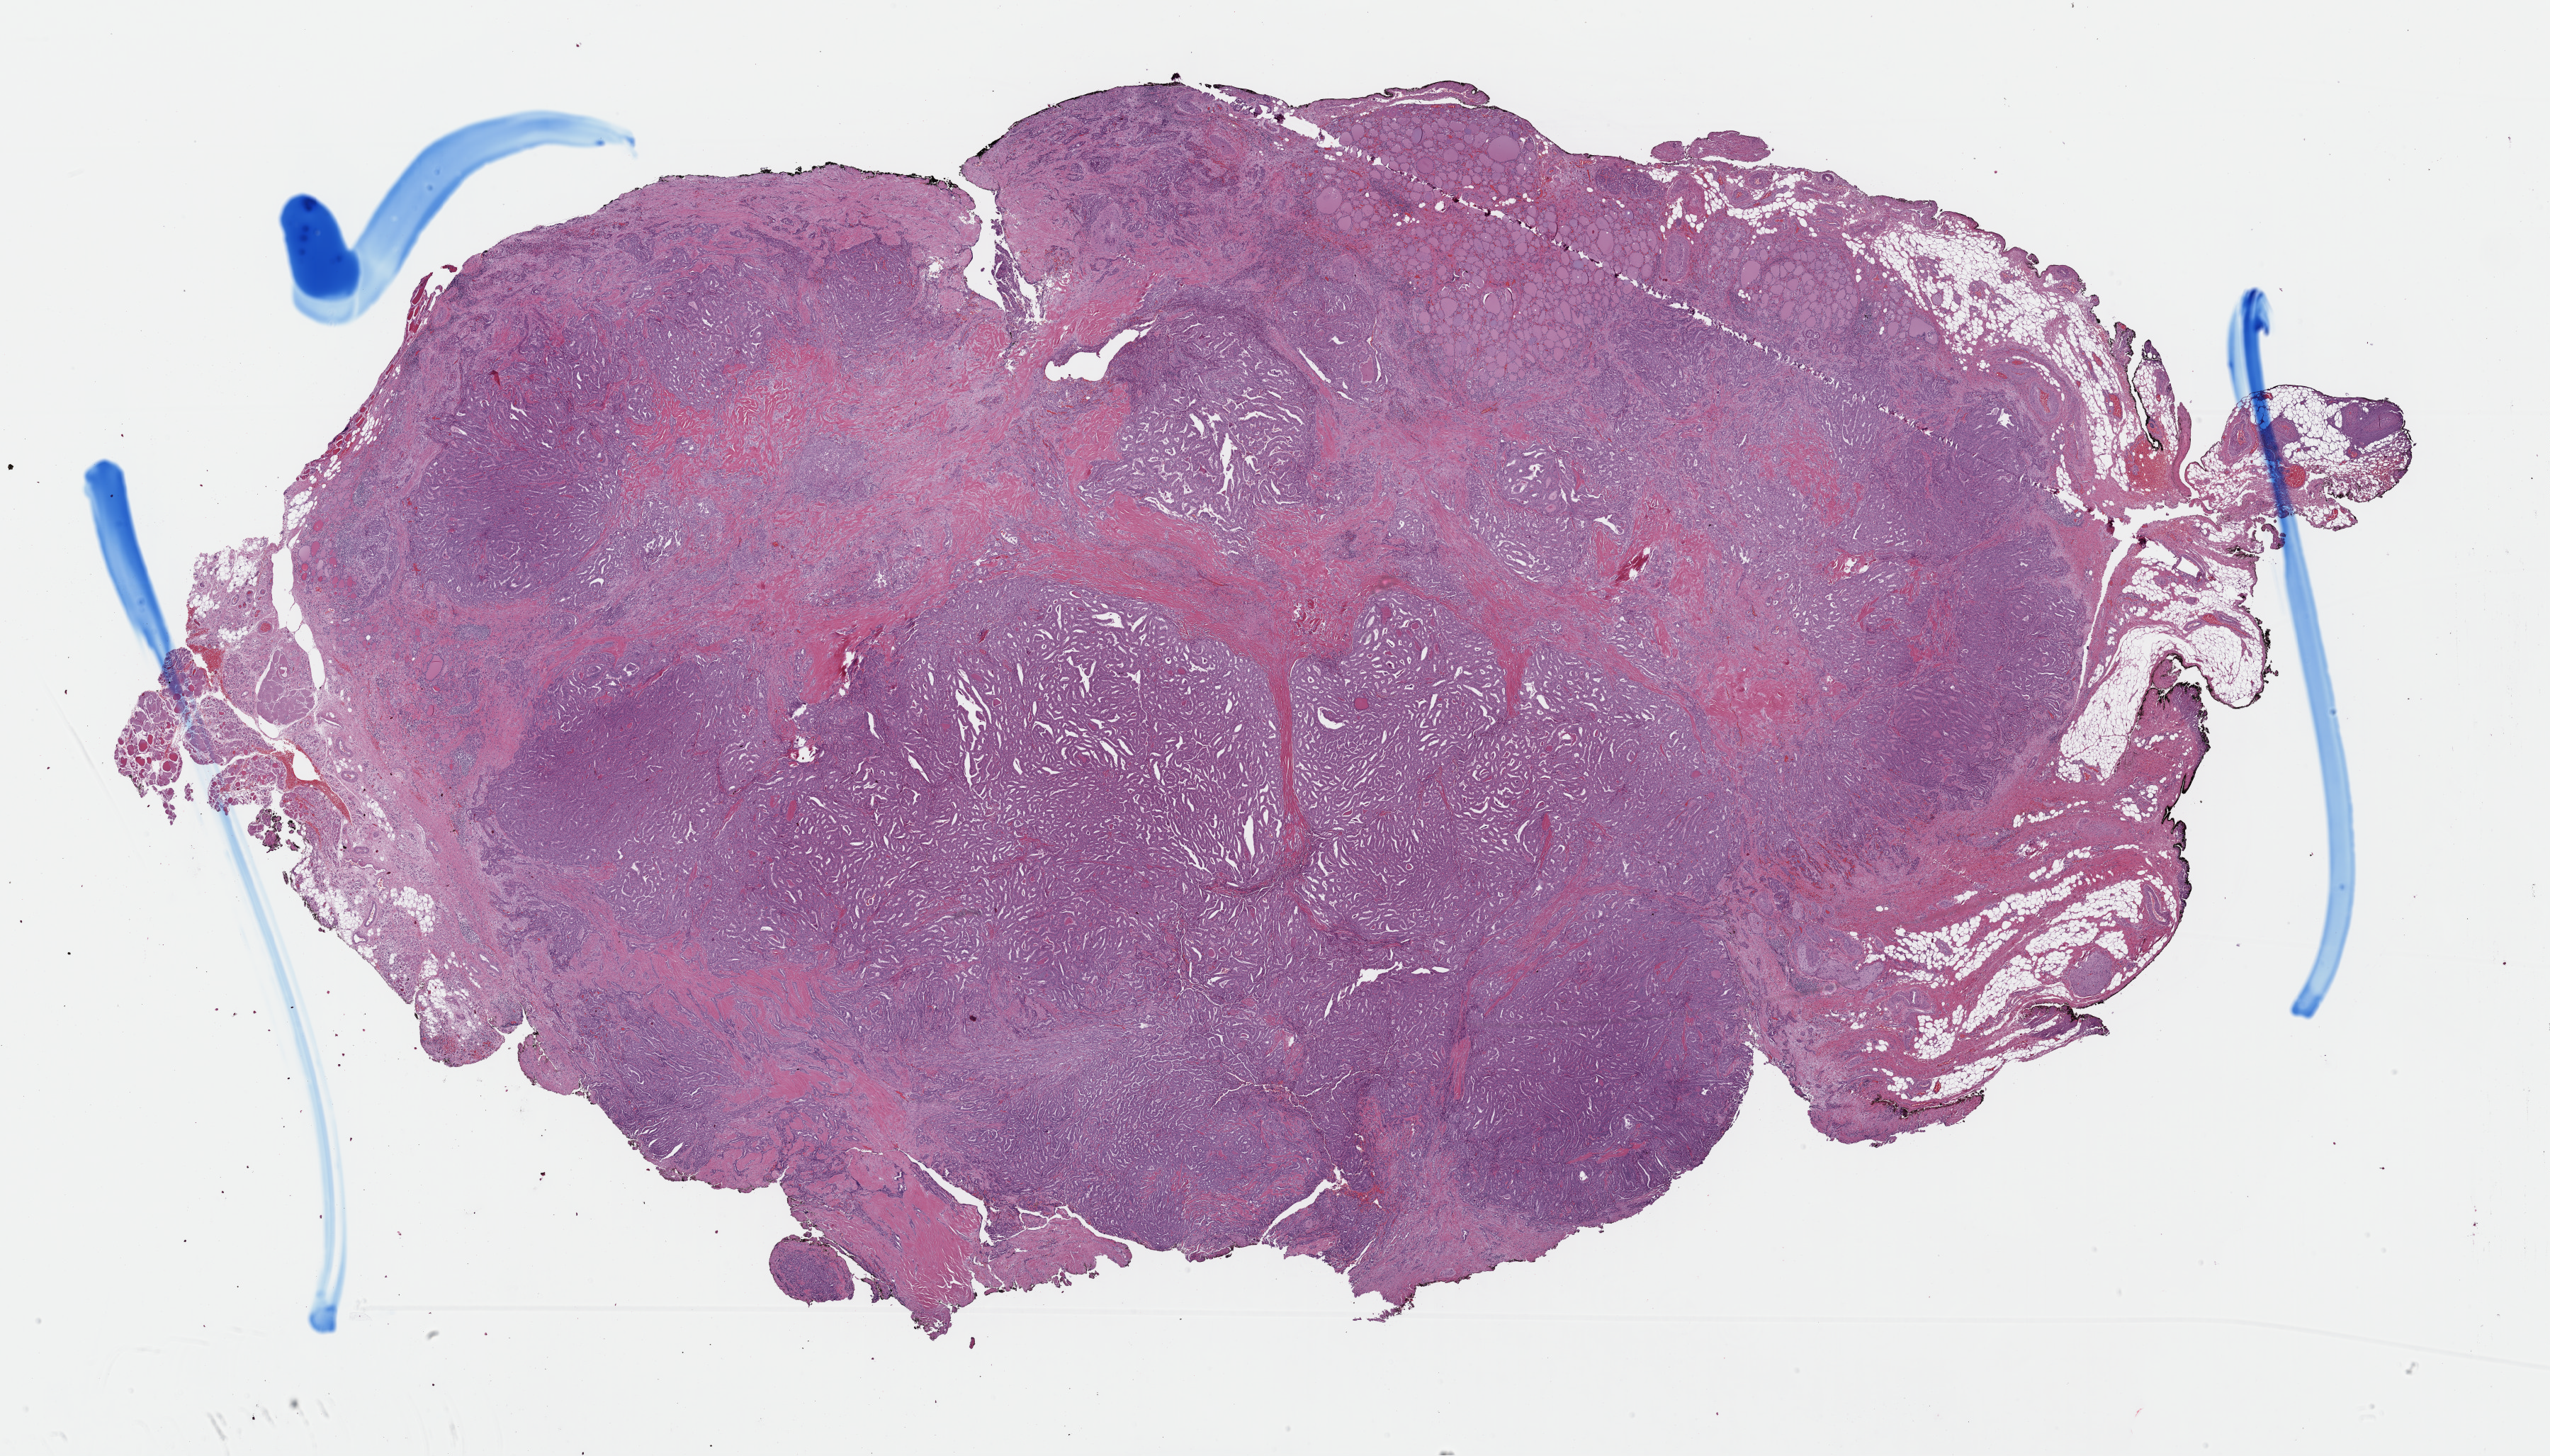
Digitized H&E-stained tissue section (whole slide), a low-resolution overview of the entire scanned area, about 28.4 x 16.2 mm (acquisition: 40x scan), formalin-fixed paraffin-embedded (FFPE) diagnostic section, primary tumour sample from the thyroid. Patient sex: female.
- AJCC pathologic stage: IVA
- histologic diagnosis: Papillary carcinoma, columnar cell (thyroid gland)
- lymph nodes positive (case pathology): 25 of 33 examined